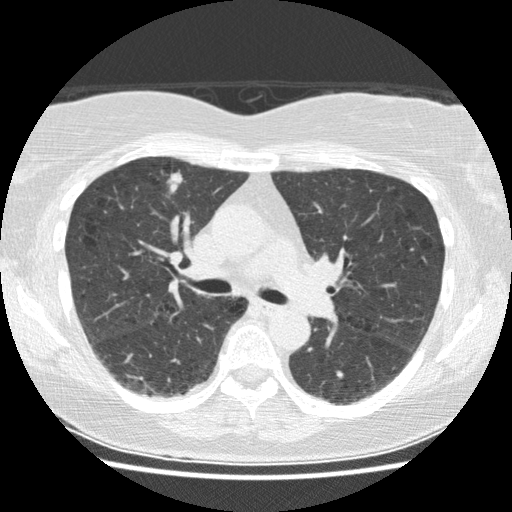
Axial slice from a low-dose chest CT screening exam, baseline screening round, lung window (W 1500 / L -600 HU), slice 63 of 155 in the series, 512 × 512 image matrix, field of view 330 × 330 mm. Female, age 63 years at enrolment. Current smoker at enrolment.
• Expert-annotated lung lesion, bounding box <147,154,193,211> (left, top, right, bottom; pixels).
• Reader record for this screening exam (exam-level; its link to the box is not recorded): non-calcified nodule or mass ≥4 mm, right upper lobe, 18 × 14 mm, spiculated (stellate) margins, soft tissue attenuation.
• Official screen result: positive, change unspecified: nodule(s) >= 4 mm or enlarging nodule(s), mass(es), or other non-specific abnormalities suspicious for lung cancer.
• Later outcome: lung cancer diagnosed 87 days after this screen — papillary adenocarcinoma, NOS, right upper lobe, well differentiated (G1), stage IA (AJCC 6th edition), 19 mm at pathology.